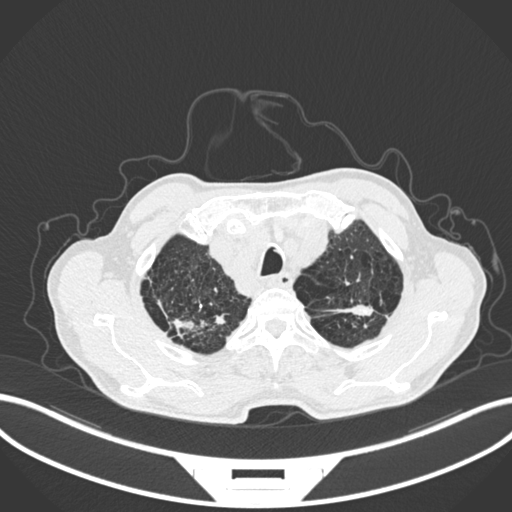
Chest CT, one axial slice. Slice 241 of 287 in the series (ordered by position). Reconstruction kernel B30f. Lung window (W 1500 / L -600 HU). 1 mm slice thickness. 512 × 512 image matrix, field of view 400 × 400 mm. Male patient, age 74 years. Case-level facts recorded for this patient, not image findings: clinical TNM (as recorded): T2a N1 M0.
Outlined on this slice (bounding box drawn by a radiologist):
- lung tumour (recorded histology: adenocarcinoma): bounding box [x1, y1, x2, y2] px = [339, 300, 383, 324]